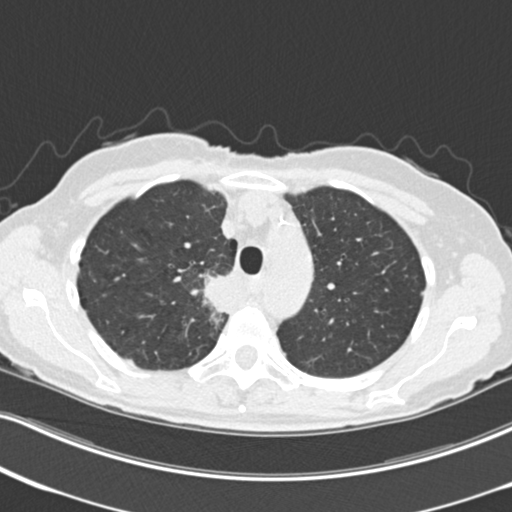
Axial slice from a low-dose chest CT screening exam. Third annual screen. Lung window (W 1500 / L -600 HU). 2 mm slice thickness. Standard (soft-tissue) reconstruction kernel (B30f). Slice 55 of 226 in the series. Female, age 68 years at enrolment. Current smoker at enrolment.
Lesion marked by an expert reader, bounding box <197,266,249,322> (left, top, right, bottom; pixels). Reader record for this screening exam (exam-level; its link to the box is not recorded): non-calcified nodule or mass ≥4 mm, right upper lobe, 31 × 29 mm, poorly defined margins, soft tissue attenuation, pre-existing on the prior screen: no.